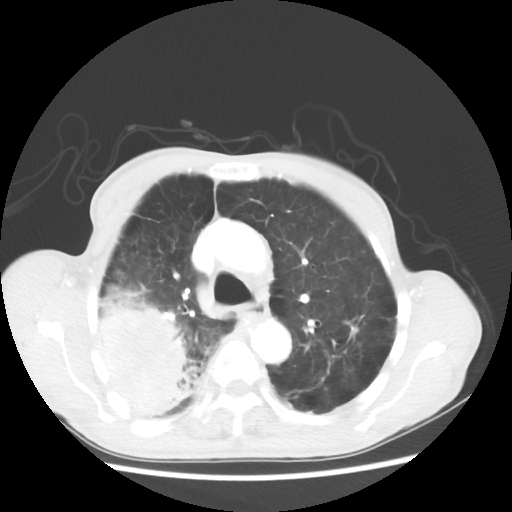
Chest CT, one axial slice. Position 38 of 58 along the scan axis. 100 kVp. Lung window (W 1500 / L -600 HU). 5 mm slice thickness. 512 × 512 image matrix, field of view 351 × 351 mm. Patient: male, 75 years. From the clinical record (not read from this slice): clinical TNM (as recorded): T4 N1 M1.
Outlined on this slice (rectangle marked by the reading radiologist):
- lung tumour (recorded histology: adenocarcinoma): bounding box (x1, y1, x2, y2) in pixels: (91, 281, 201, 419)